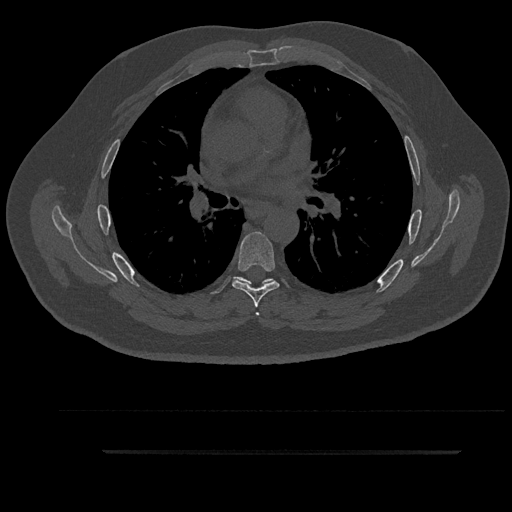
CT including the spine, one axial slice; 120 kVp; bone window (W 1800 / L 400 HU); 512 × 512 image matrix, field of view 432 × 432 mm. Patient: male, 63 years. Case-level facts recorded for this patient, not image findings: primary cancer: renal.
Annotated regions visible in this slice (semi-automatically segmented with operator editing):
- T5 vertebra: bounding box [x1, y1, x2, y2] px = [235, 277, 274, 316]
- T6 vertebra: [232, 231, 279, 308]
- T7 vertebra: [242, 278, 275, 284]